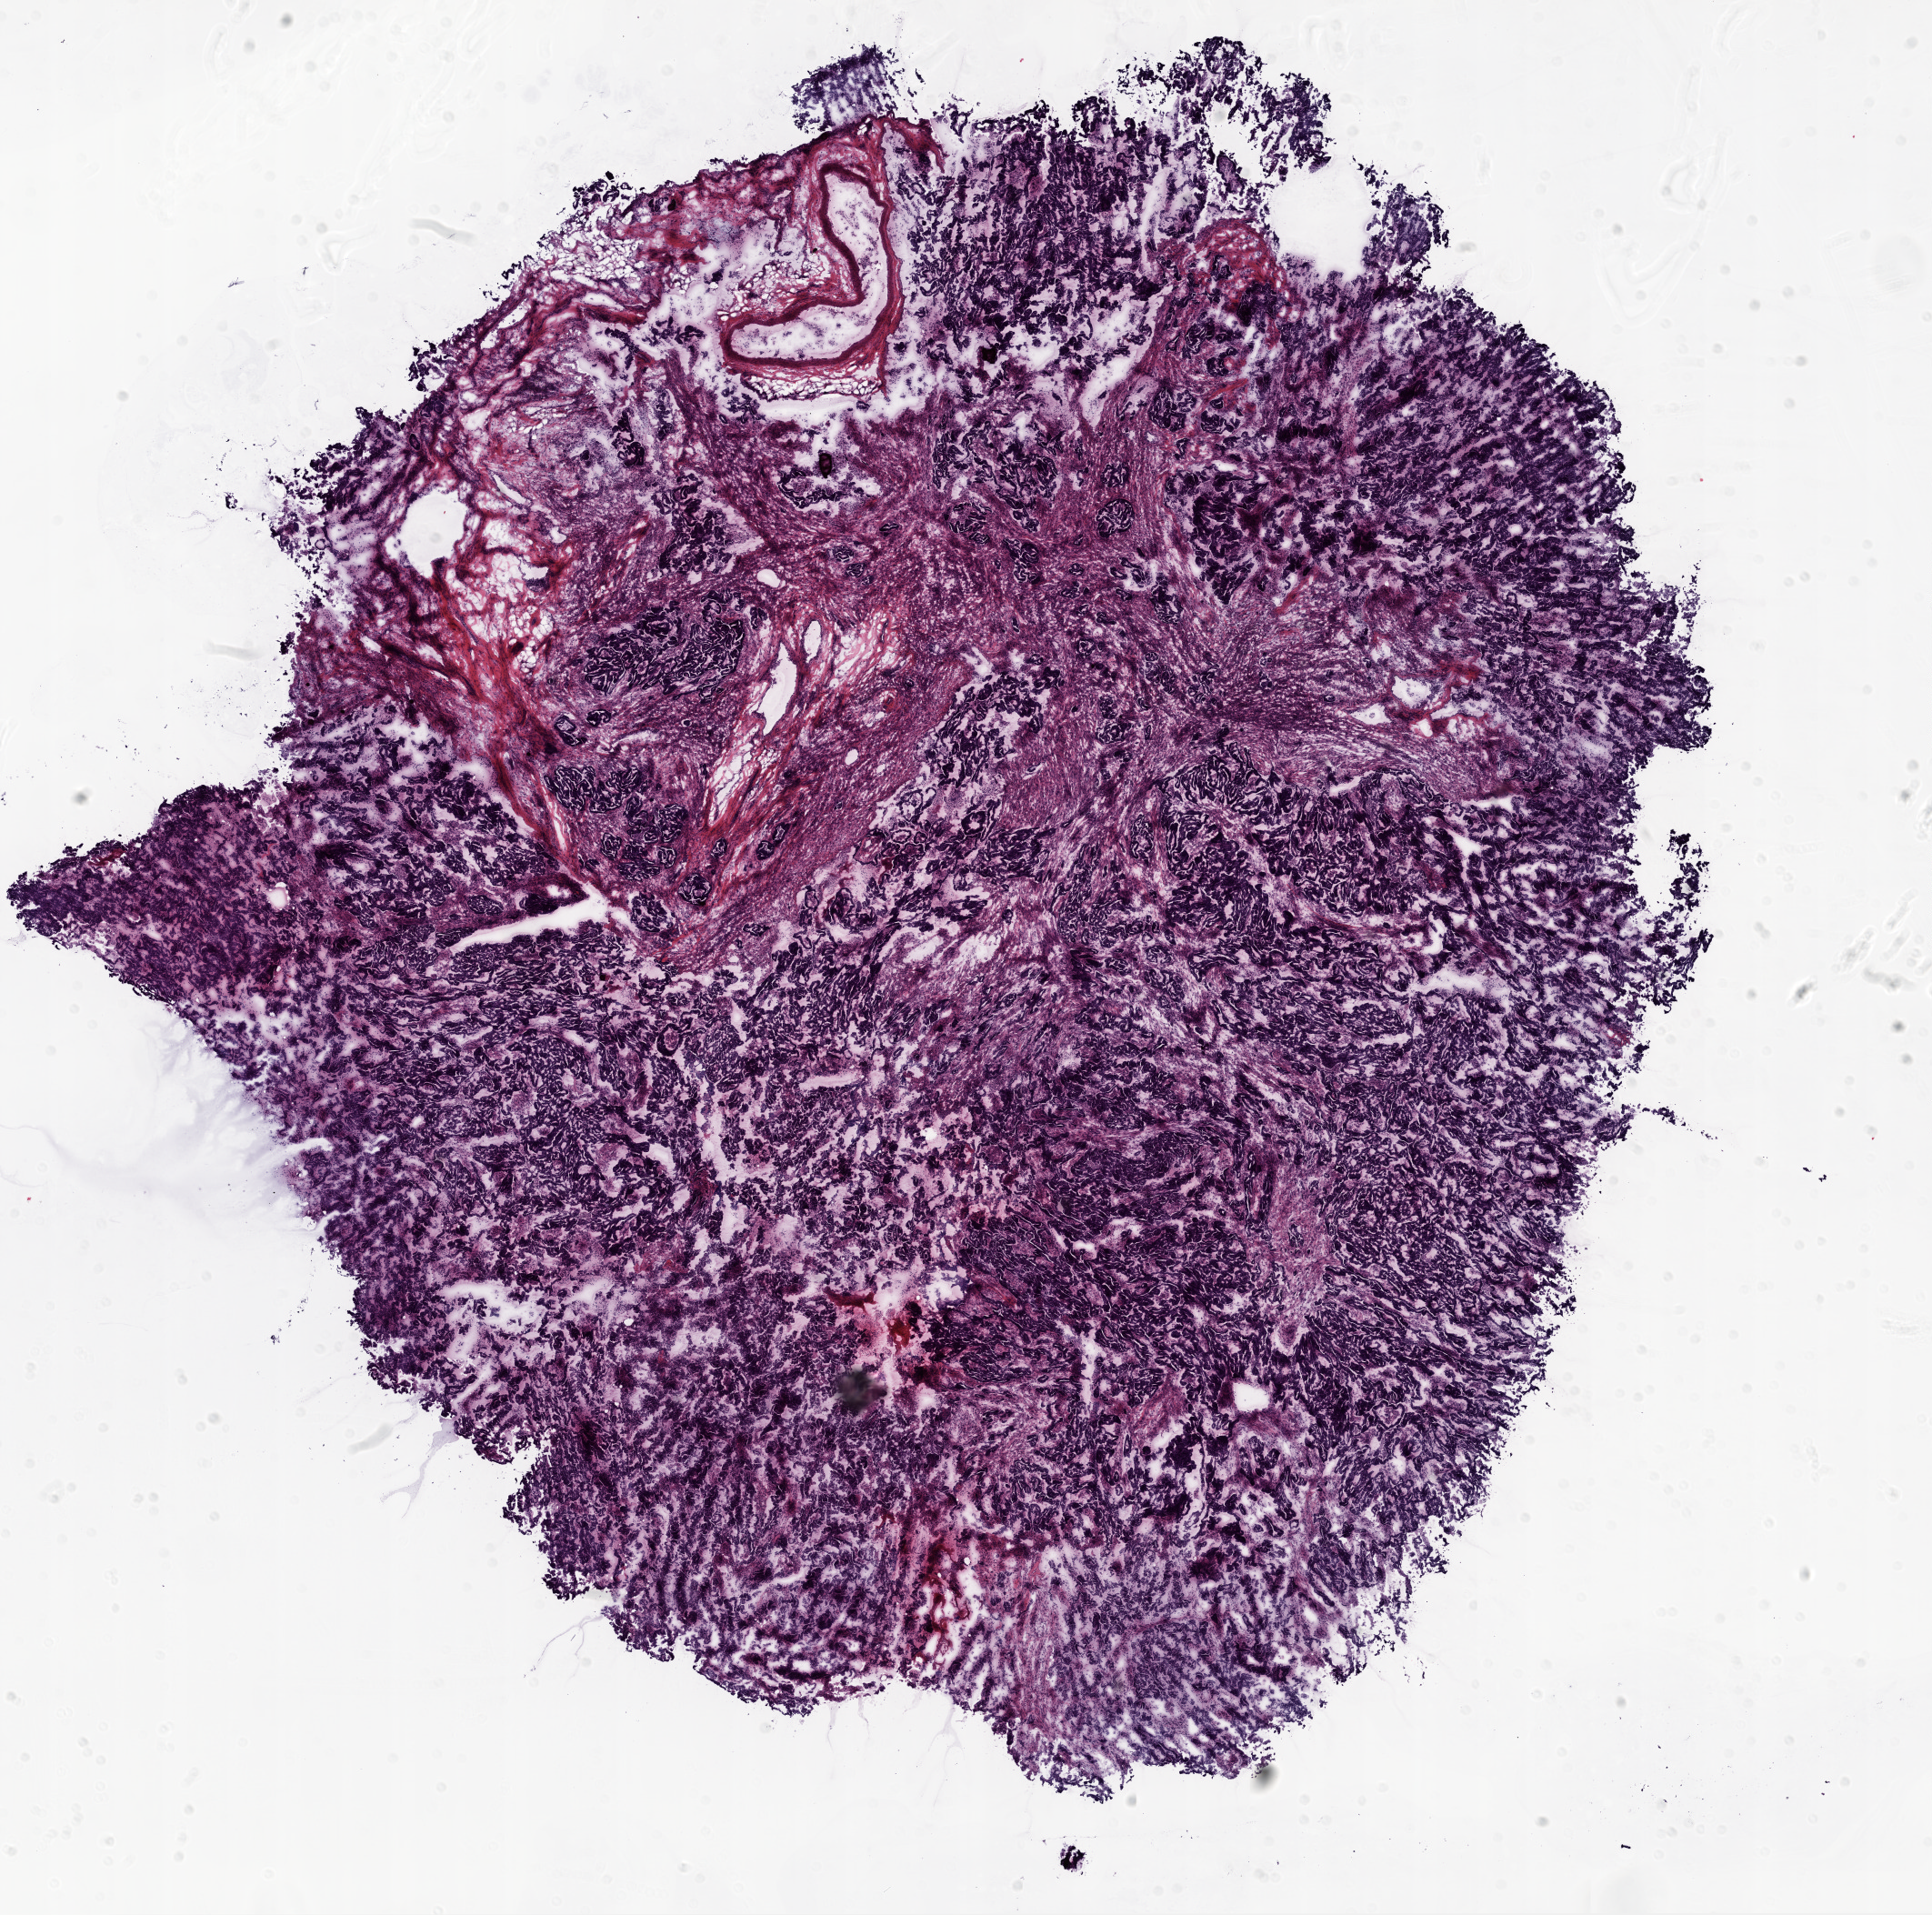
Whole-slide histology image, Hematoxylin and eosin (H&E) stained — whole scanned area (about 17.1 x 16.9 mm, acquisition: 20x scan) shown as a low-resolution overview; frozen section; ovary, primary tumour sample. Female patient; age at initial diagnosis 52 years. Histologic grade: G2 (moderately differentiated). Slide review estimates, as recorded: tumour cells 85%, tumour nuclei 90%, normal cells 0%, stromal cells 15%, necrosis 0%. Infiltration values recorded for this section: lymphocyte infiltration 65%, monocyte infiltration 5%, neutrophil infiltration 30%.
FIGO stage: IV. Histologic diagnosis: Serous cystadenocarcinoma, NOS.